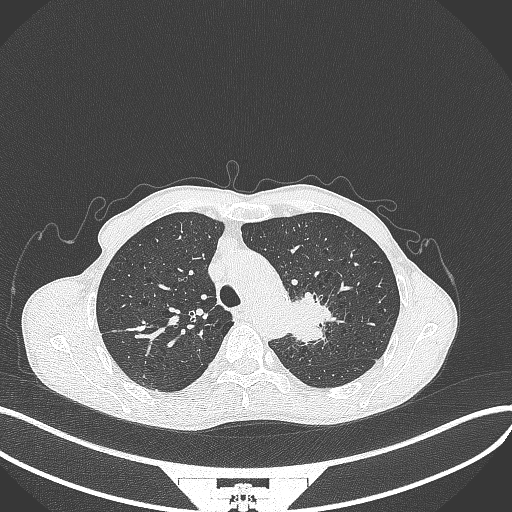
Chest CT, one axial slice; slice 314 of 386 in the series (ordered by position); 120 kVp; lung window (W 1500 / L -600 HU); 1 mm slice thickness; 512 × 512 image matrix, field of view 400 × 400 mm. Male patient, age 65 years. Case-level facts recorded for this patient, not image findings: clinical TNM (as recorded): T2b N0 M0.
Outlined on this slice (rectangle marked by the reading radiologist):
- lung tumour (recorded histology: adenocarcinoma): bounding box [x1, y1, x2, y2] px = [286, 292, 336, 346]